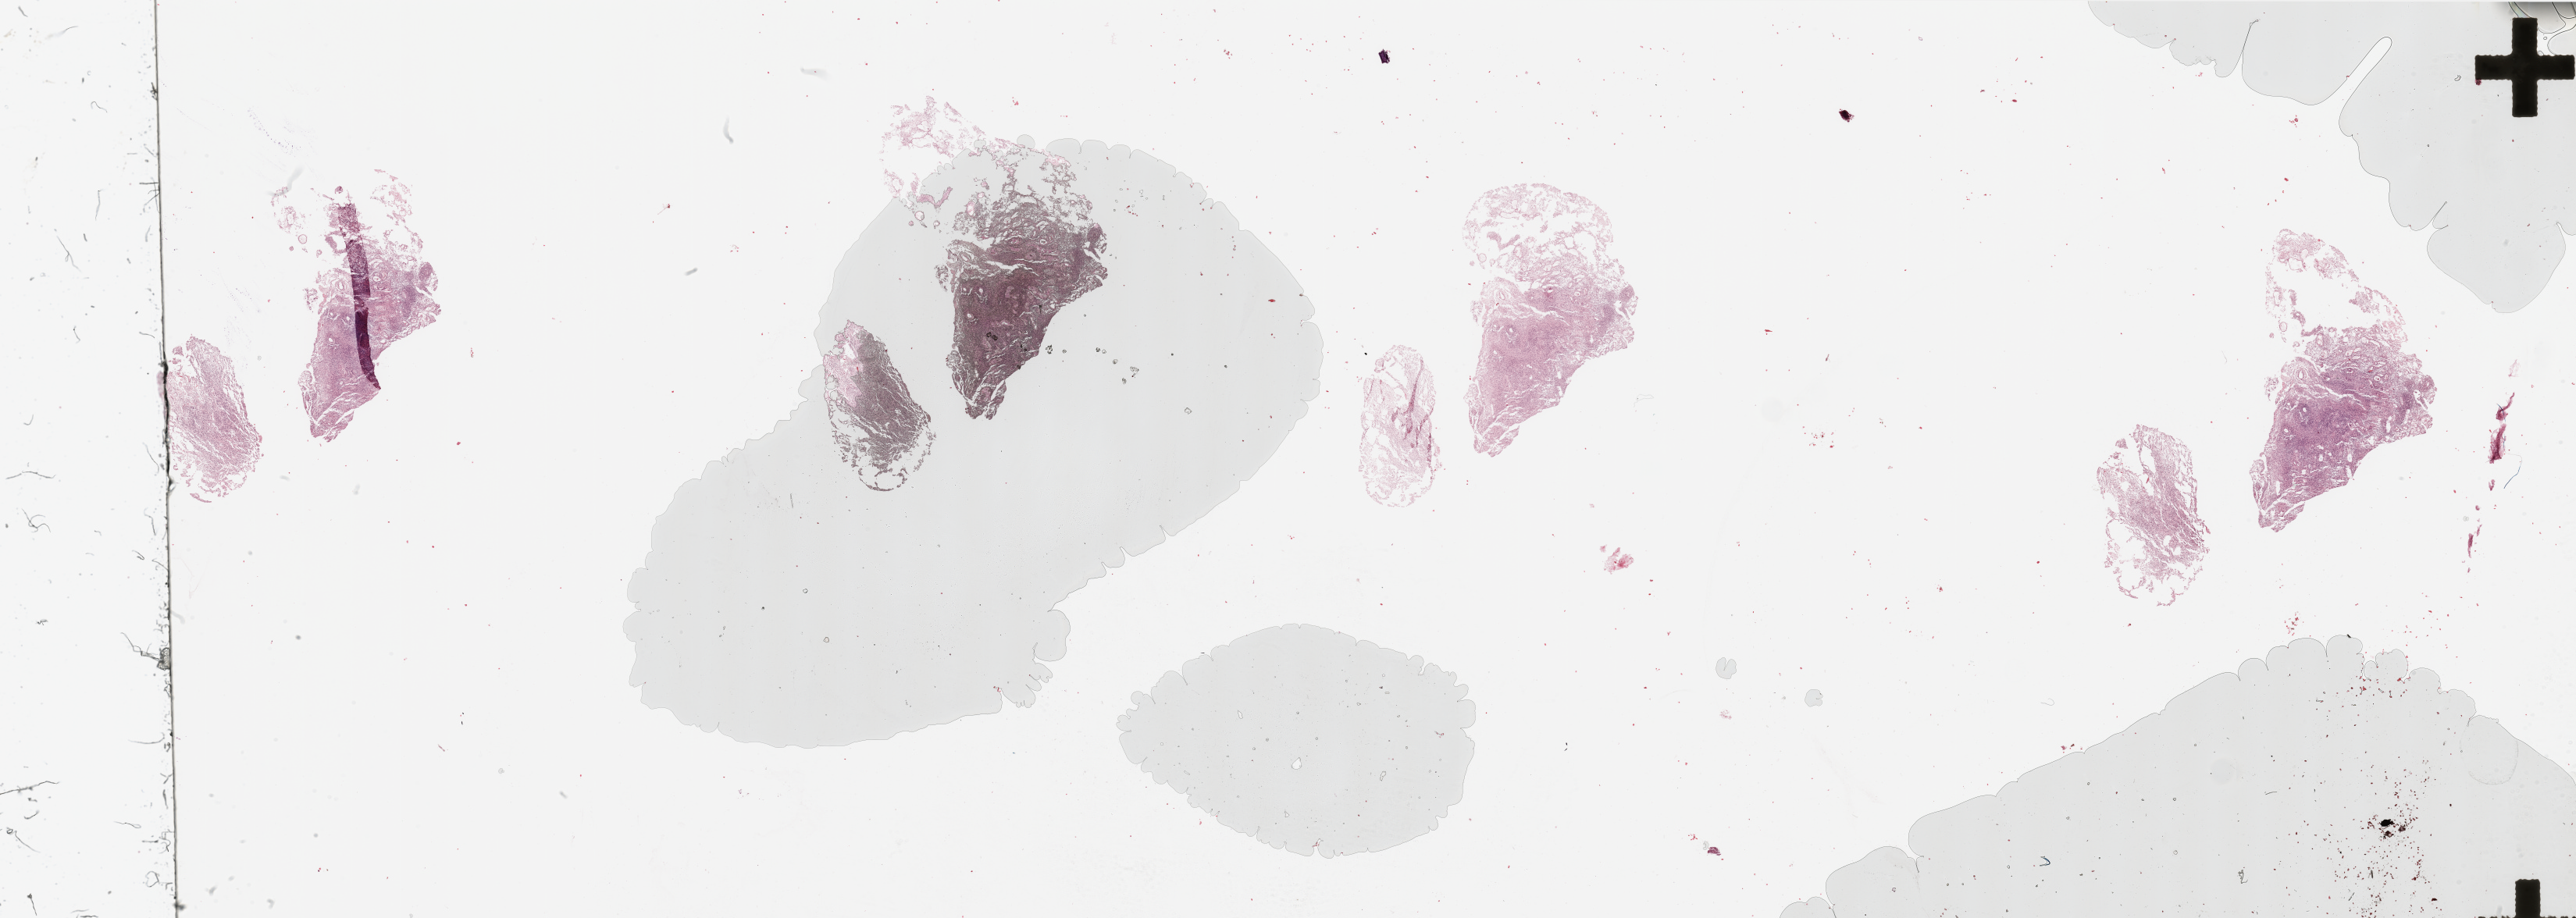
Digitized H&E tissue section (whole slide) — whole scanned area (about 52.2 x 18.6 mm, acquisition: 20x scan) shown as a low-resolution overview. Brain, tumour tissue. Male, 40 y/o.
Histologic diagnosis: Glioblastoma.